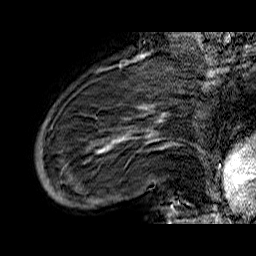
Breast MRI (dynamic contrast-enhanced), one sagittal slice. Slice 12 of 60 in the series (ordered by position). Dynamic contrast-enhanced series, time point 2 of 6 at this slice position (early post-contrast). 1.5 T. TE 6.5 ms, TR 32.9 ms. 4 mm slice thickness. 256 × 256 image matrix, field of view 200 × 200 mm. Female patient. From the clinical record (not read from this slice): setting: breast cancer imaged before/during neoadjuvant chemotherapy; receptor status: HR-positive, HER2-negative.
Structures marked on this image (semi-automatic segmentation, software-assisted and operator-edited):
- analysis volume of interest (the breast-tissue region the enhancement analysis was run in; not a lesion): bounding box <36,74,176,210> (left, top, right, bottom; pixels)
- tumour enhancement mask (voxels above the 100 % enhancement threshold inside the analysis volume of interest): <40,107,168,156>